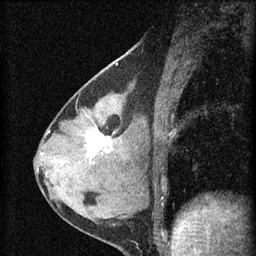
Breast MRI (dynamic contrast-enhanced), one sagittal slice; slice 27 of 60 in the series (ordered by position); dynamic contrast-enhanced series, image 2 of 4 at this slice position (ordered by acquisition); 1.5 T; TE 4.2 ms, TR 8.2 ms; 2 mm slice thickness; 256 × 256 image matrix, field of view 180 × 180 mm. Patient: female, 37 years.
Structures marked on this image (semi-automatic segmentation, software-assisted and operator-edited):
- analysis volume of interest (the breast-tissue region the enhancement analysis was run in; not a lesion): bounding box (x1, y1, x2, y2) in pixels: (77, 116, 127, 175)
- tumour enhancement mask (voxels above the 70 % enhancement threshold inside the analysis volume of interest): (86, 130, 111, 154)